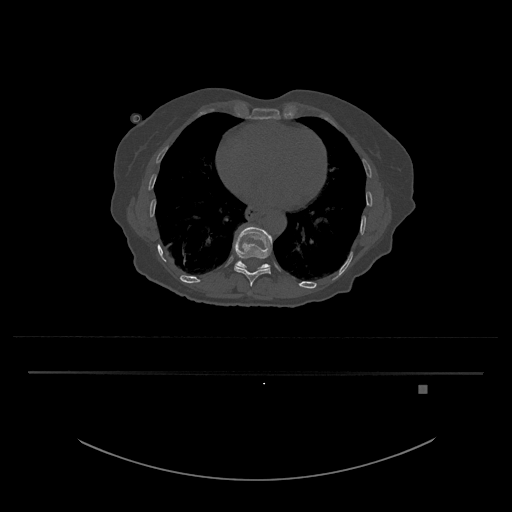
CT including the spine, one axial slice; position 701 of 797 along the scan axis; reconstruction kernel Br40s/3; 120 kVp; bone window (W 1800 / L 400 HU); 0.5 mm slice thickness; 512 × 512 image matrix, field of view 500 × 500 mm. Patient: female, 57 years. From the clinical record (not read from this slice): primary cancer: cervical.
Structures marked on this image (semi-automatically segmented with operator editing):
- T10 vertebra: box from (x=233, y=226) to (x=272, y=287) px
- T11 vertebra: (x=235, y=258)–(x=271, y=270)